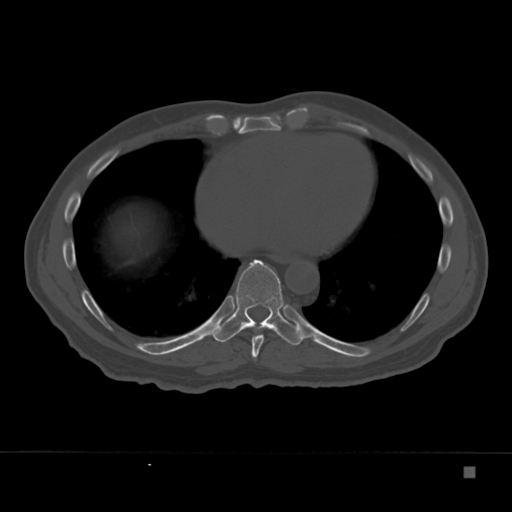
CT including the spine, one axial slice; position 195 of 332 along the scan axis; bone window (W 1800 / L 400 HU); 1.5 mm slice thickness; 512 × 512 image matrix, field of view 389 × 389 mm. Male patient, age 72 years. From the clinical record (not read from this slice): primary cancer: skeletal.
Structures marked on this image (semi-automatic segmentation, software-assisted and operator-edited):
- T8 vertebra: bounding box <251,334,265,359> (left, top, right, bottom; pixels)
- T9 vertebra: <213,259,305,346>